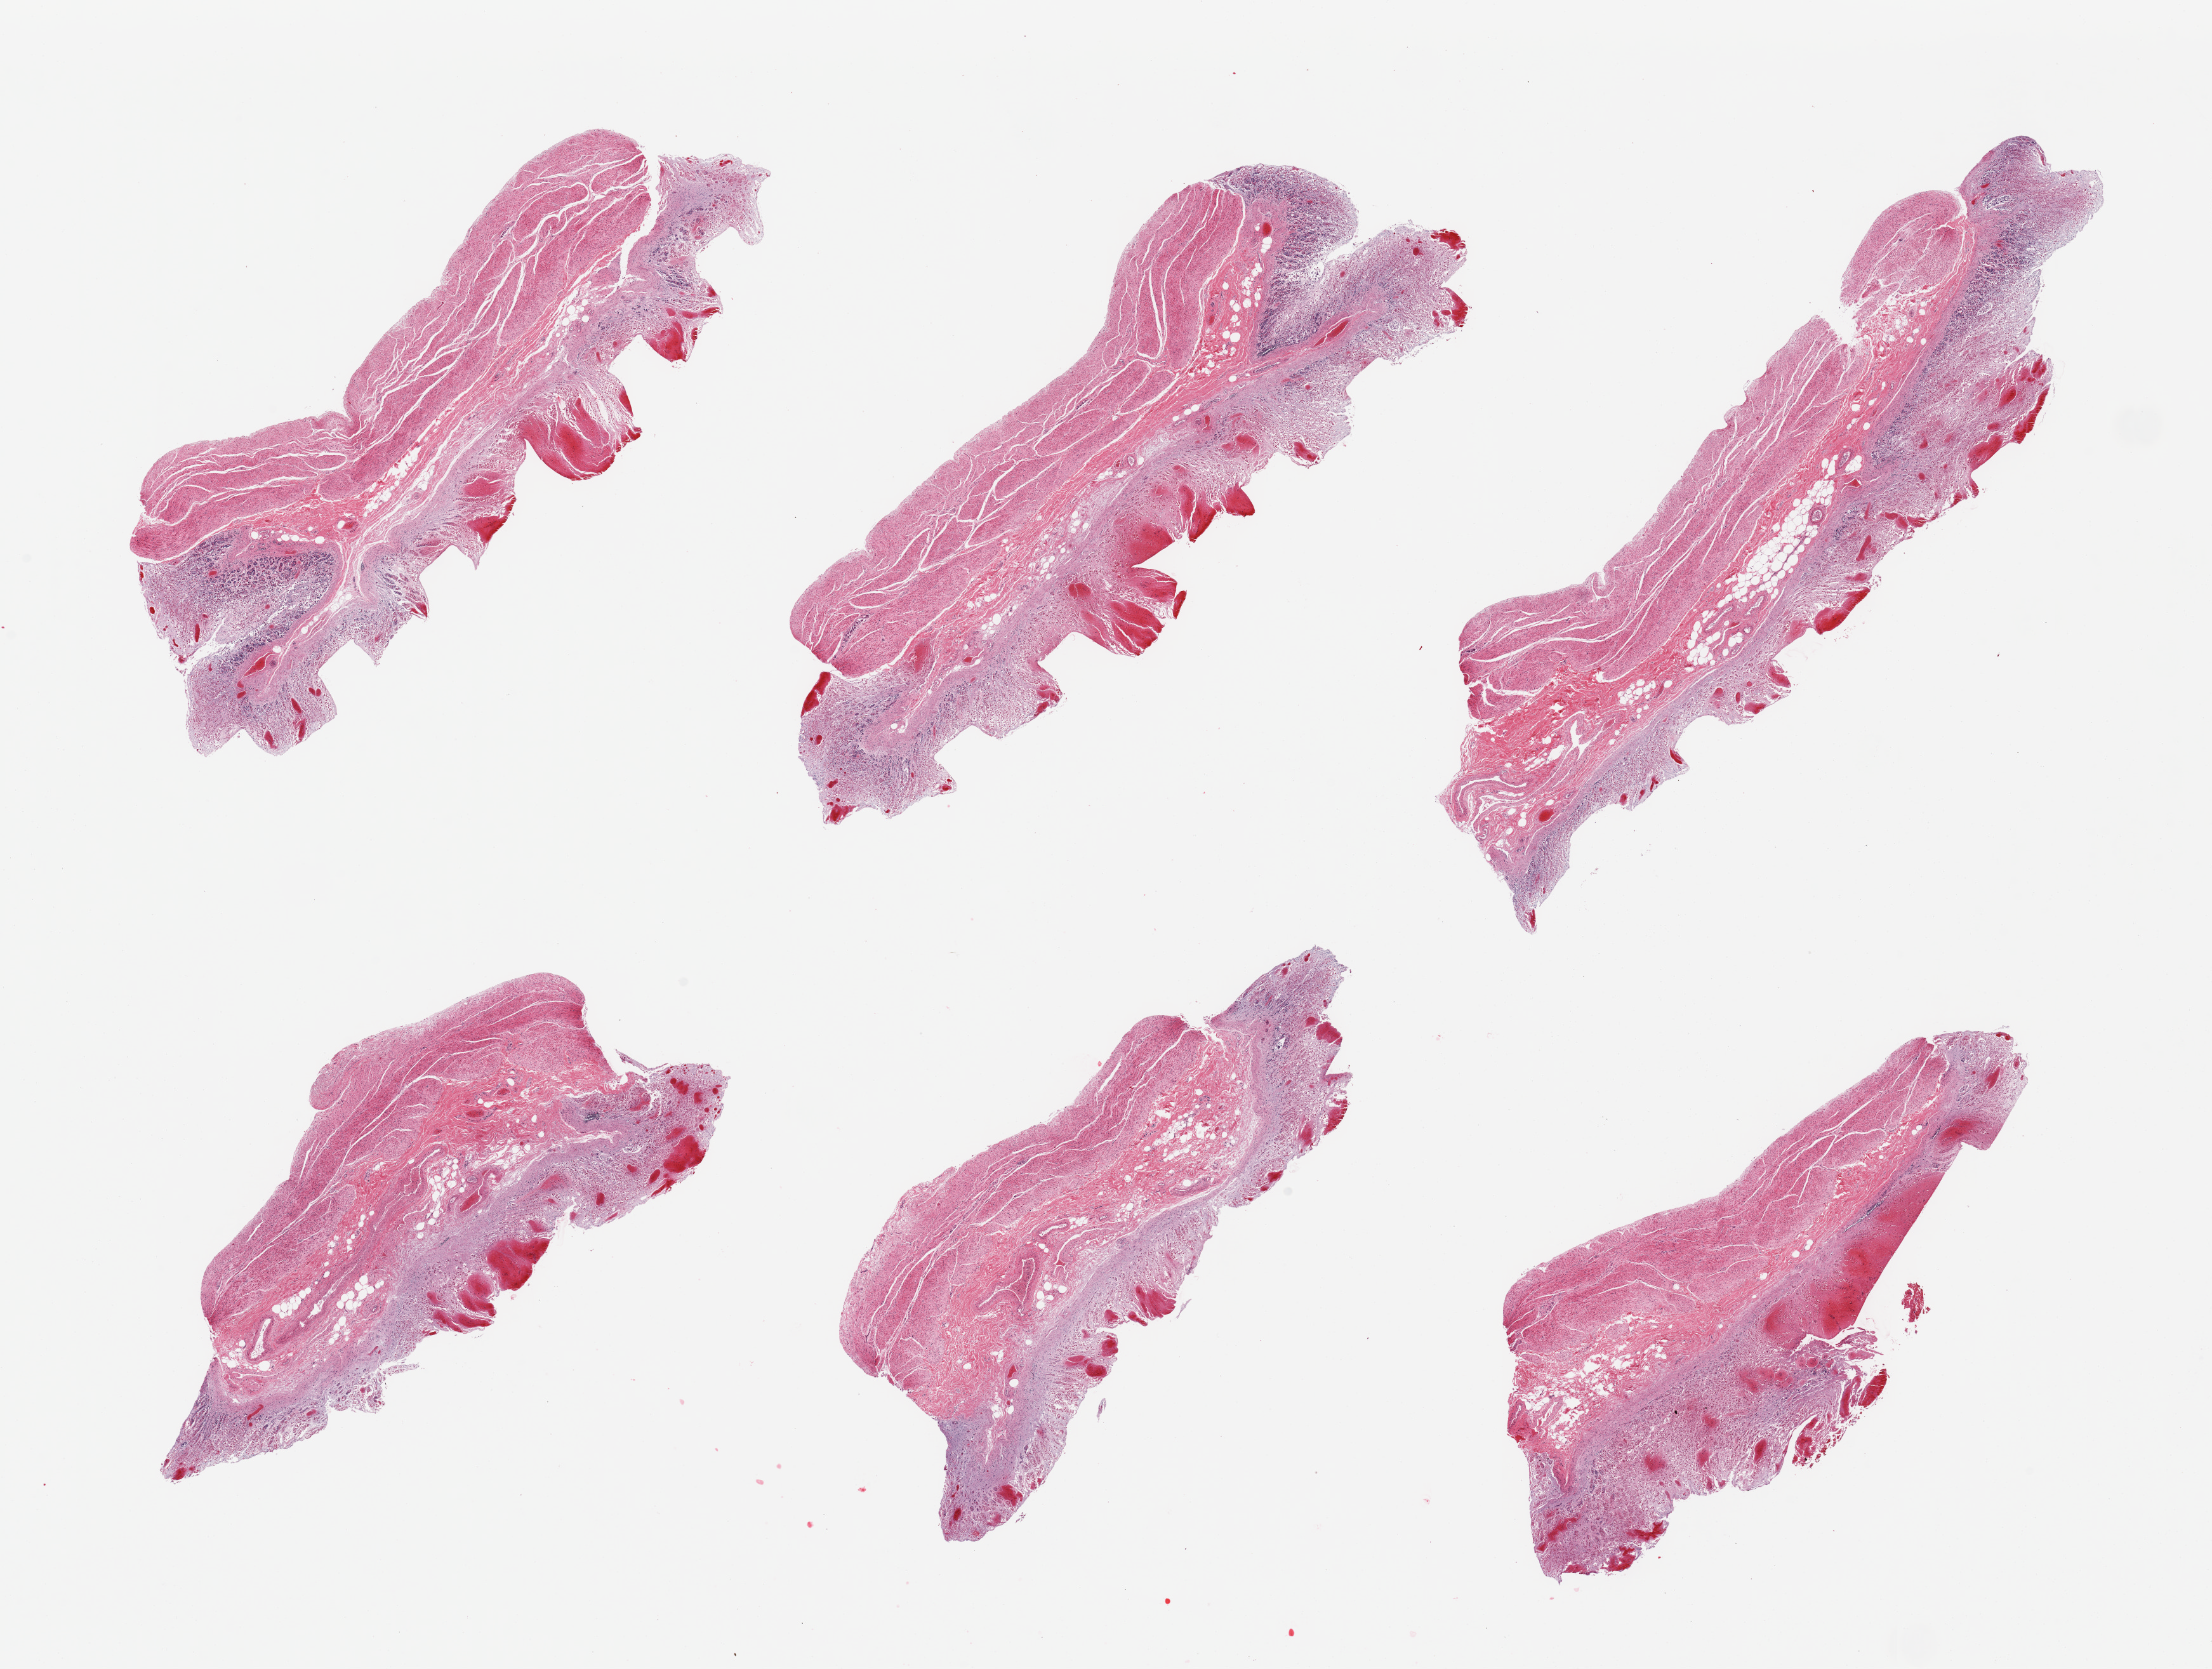
Digitized haematoxylin and eosin-stained section — a low-resolution overview of the entire scanned area, about 27.6 x 20.8 mm (from a 20x scan), PAXgene-fixed paraffin-embedded (PFPE) section, target tissue: stomach, tissue donor sample.
Reviewer comment on this tissue sample: 6 pieces, mucosa up to ~50-60% thickness but markedly autolyzed.